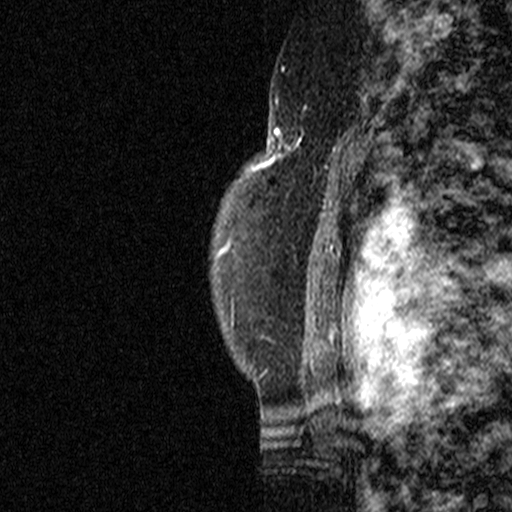
Breast MRI (dynamic contrast-enhanced), one sagittal slice; position 35 of 44 along the scan axis; dynamic contrast-enhanced study with each time point stored as its own series, time point 2 of 3 at this slice position (early post-contrast, ordered by acquisition time); 1.5 T; TE 4.5 ms, TR 11 ms; 3 mm slice thickness; 512 × 512 image matrix, field of view 200 × 200 mm. Female patient, age 49 years. Case-level facts recorded for this patient, not image findings: setting: breast cancer imaged before/during neoadjuvant chemotherapy; receptor status: triple-negative.
Annotated regions visible in this slice (semi-automatically segmented with operator editing):
- analysis volume of interest (the breast-tissue region the enhancement analysis was run in; not a lesion): bounding box (x1, y1, x2, y2) in pixels: (254, 112, 347, 207)
- tumour enhancement mask (voxels above the 90 % enhancement threshold inside the analysis volume of interest): (254, 118, 340, 207)